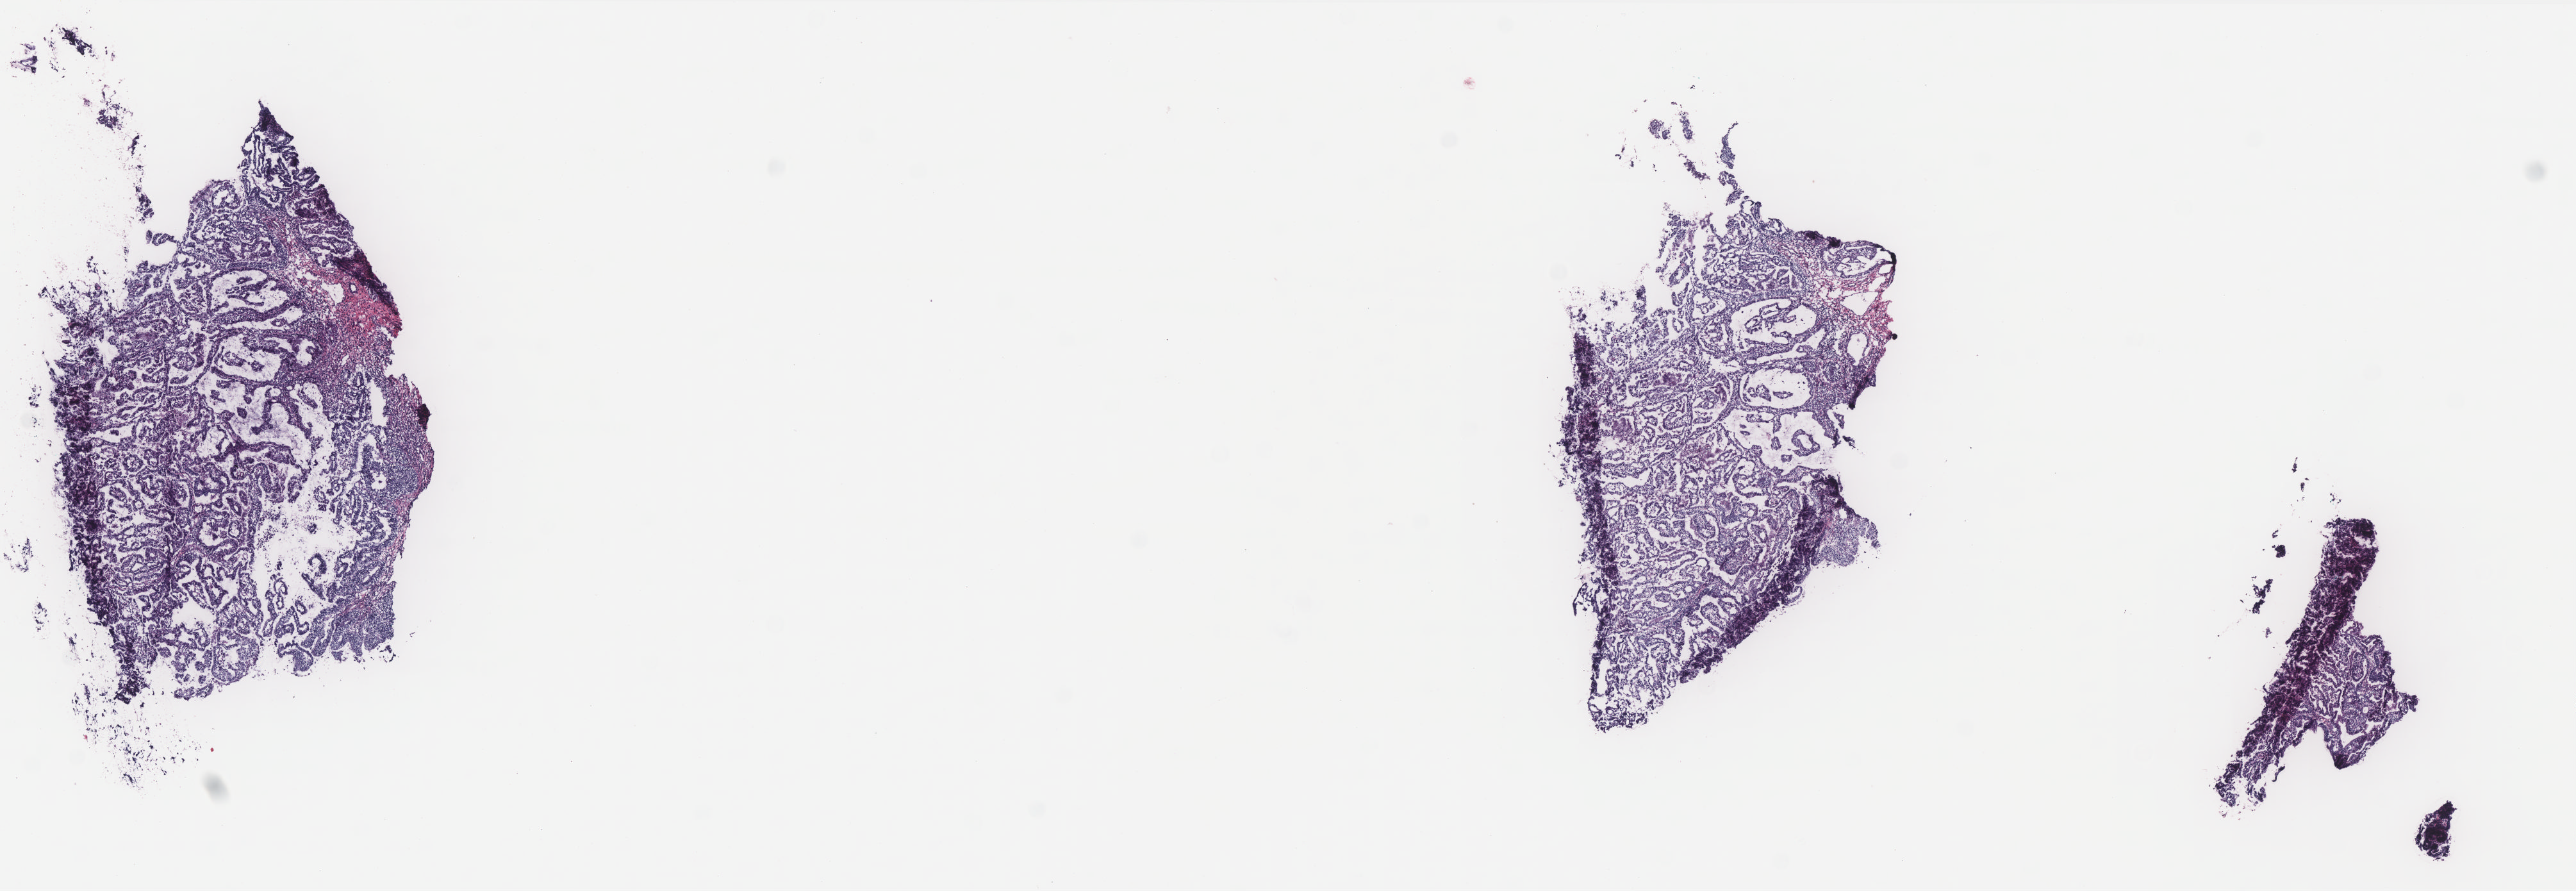
Digitized Hematoxylin and eosin (H&E) stained tissue section (whole slide), a low-resolution overview of the entire scanned area, about 16.1 x 5.6 mm (from a 40x scan); frozen section from the top of the tissue portion; uterus, primary tumour sample. Patient: female, age at initial diagnosis 68 years. Histologic grade: G1 (well differentiated). Slide review estimates, as recorded: tumour cells 90%, tumour nuclei 100%, normal cells 0%, stromal cells 10%, necrosis 0%. Inflammatory infiltration, as recorded: lymphocyte infiltration 0%, monocyte infiltration 20%, neutrophil infiltration 0%.
Histologic diagnosis: Endometrioid adenocarcinoma, NOS (endometrium). FIGO stage: IB.